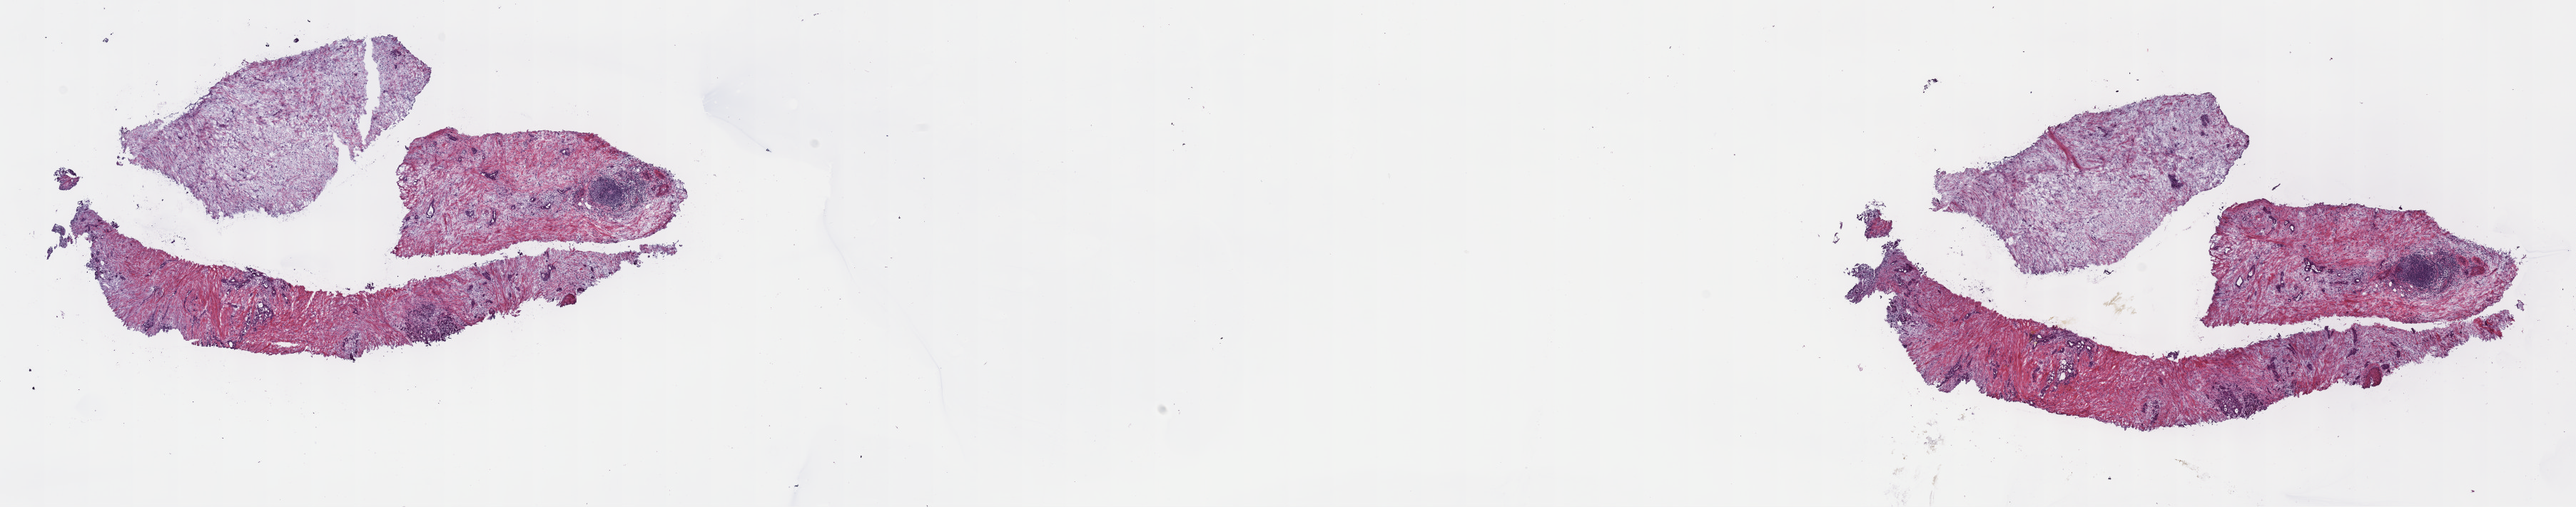
Digitized H&E-stained tissue section (whole slide), whole scanned area (about 29.2 x 5.8 mm) shown as a low-resolution overview; frozen section from the top of the tissue portion; pancreas, primary tumour sample. Patient: male, age at initial diagnosis 56 years. Histologic grade: G2 (moderately differentiated). Composition of this section per pathologist review: tumour cells 100%, tumour nuclei 20%, normal cells 0%, stromal cells 0%, necrosis 0%. Inflammatory infiltration, as recorded: lymphocyte infiltration 5%, monocyte infiltration 0%, neutrophil infiltration 0%.
* histologic diagnosis: Infiltrating duct carcinoma, NOS
* AJCC pathologic stage: IIB